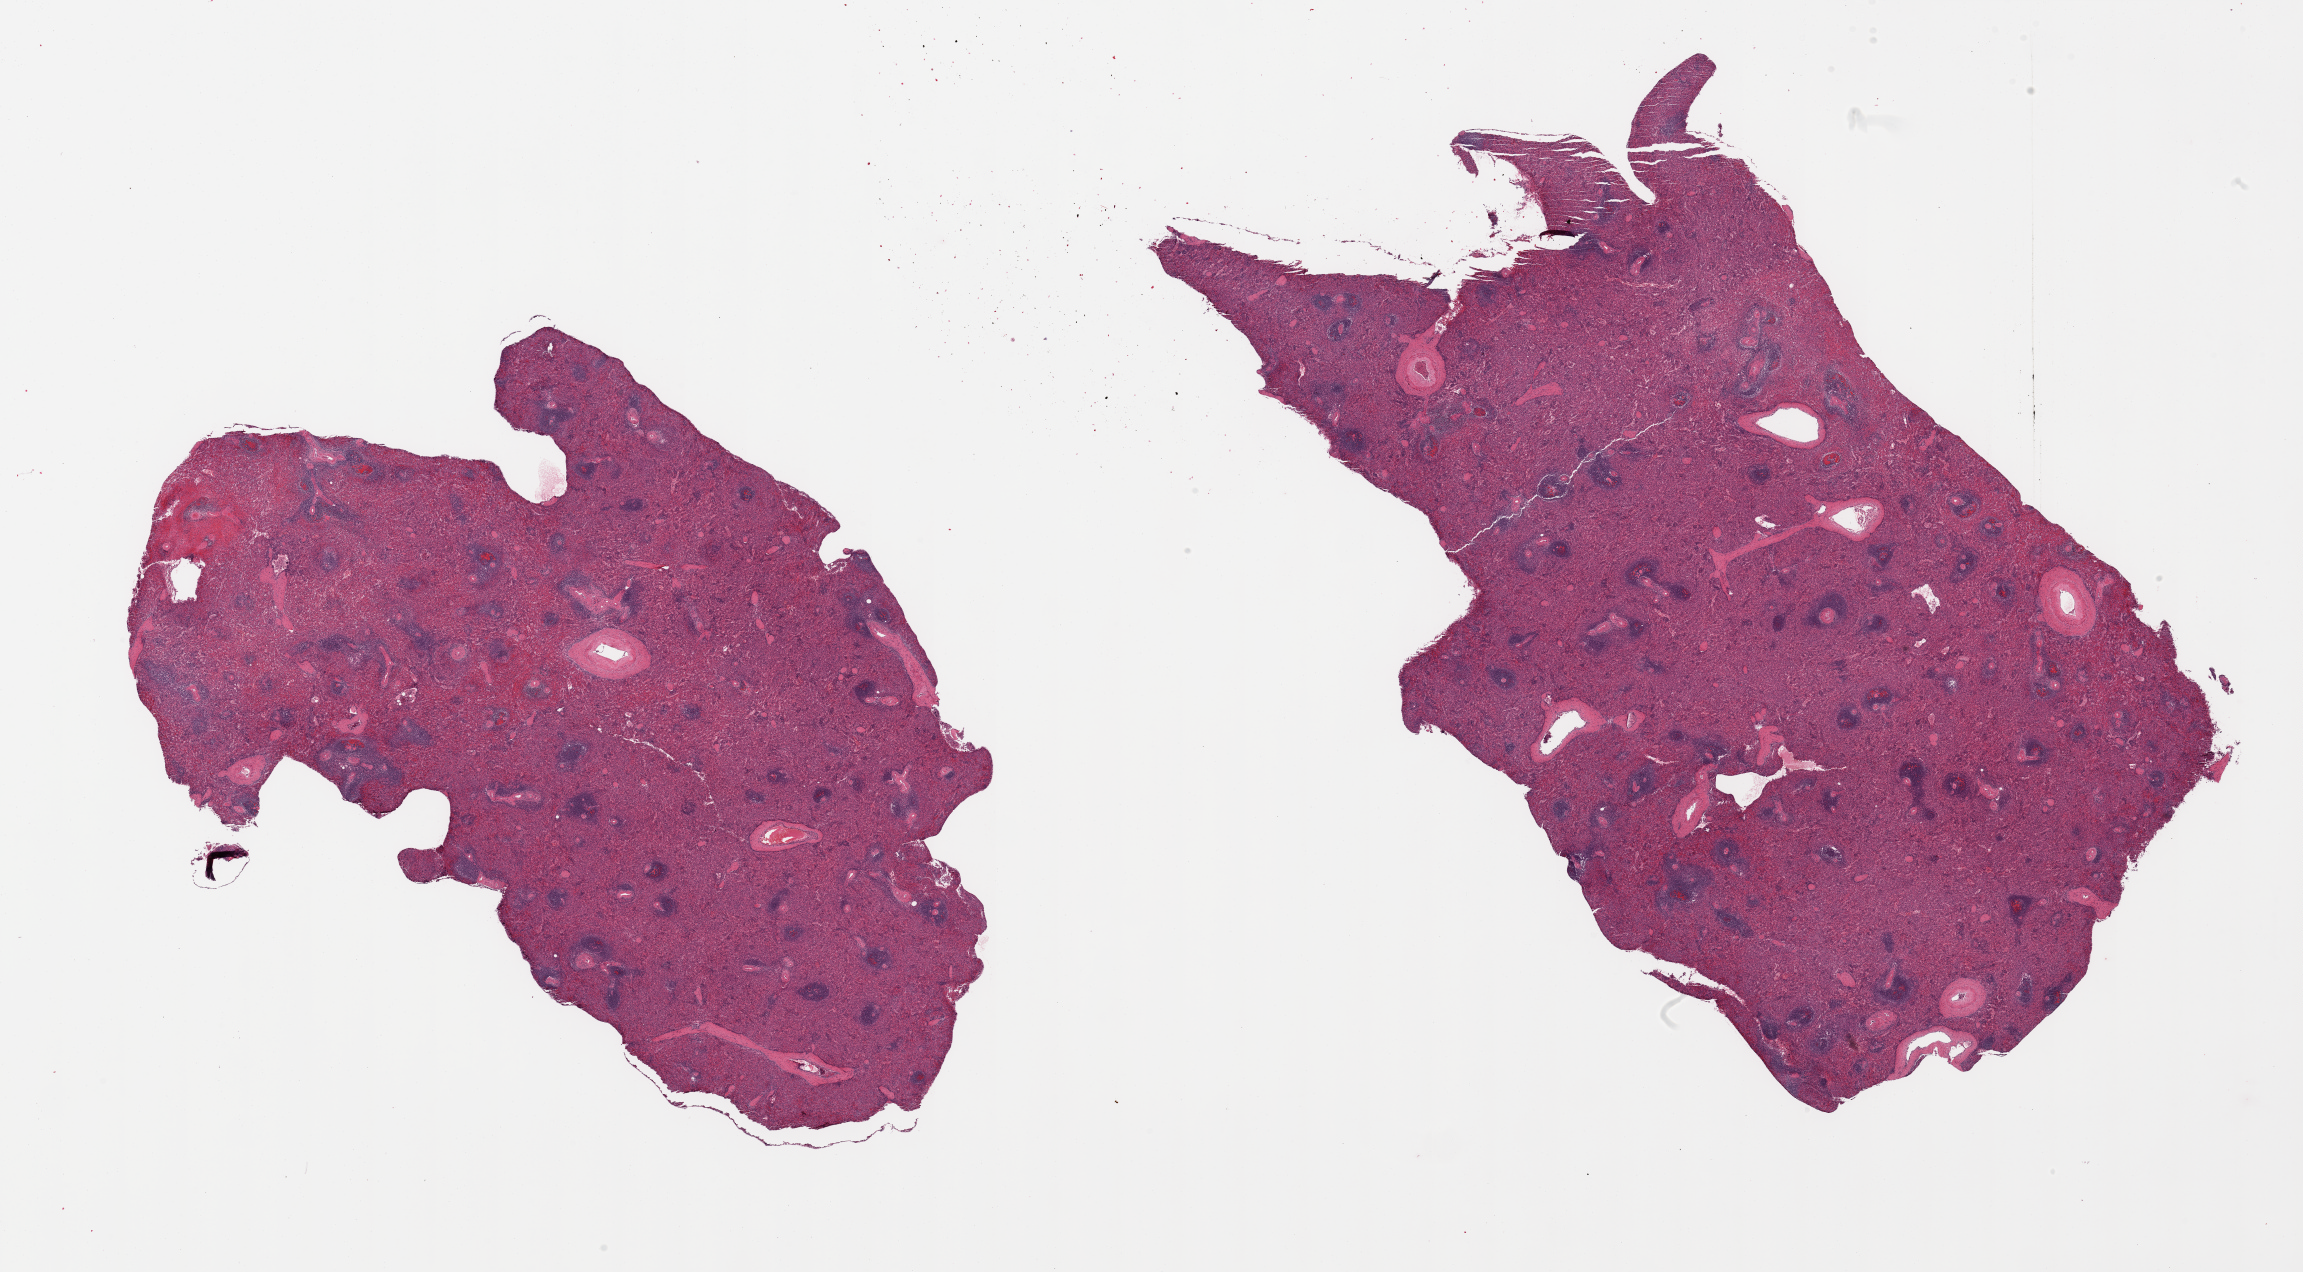
Whole-slide image, hematoxylin and eosin (H&E) stain, brightfield — a low-resolution overview of the entire scanned area, about 36.4 x 20.1 mm, PAXgene-fixed, paraffin-embedded tissue, sampled site (target tissue): spleen, tissue donor sample. Female donor.
Reviewer comment on this tissue sample: 2 pieces, no abnormalities.